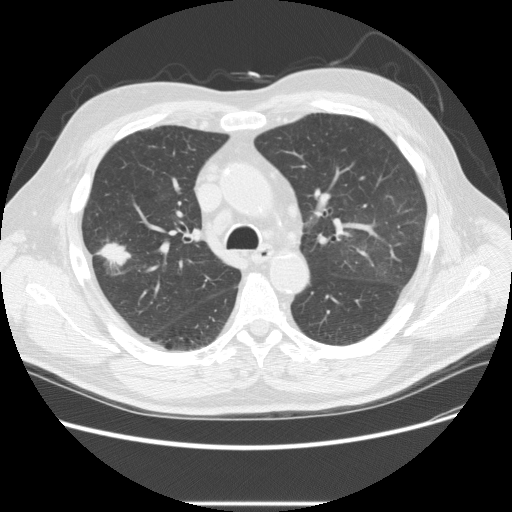
Low-dose screening chest CT, one axial slice. Slice 154 of 233 in the series (ordered by position). 120 kVp. Lung window (W 1500 / L -600 HU). 2.5 mm slice thickness. 512 × 512 image matrix, field of view 380 × 380 mm.
Outlined on this slice (expert manual segmentation):
- lesion 2 (tumor, upper lobe of right lung): box from (x=97, y=241) to (x=131, y=269) px